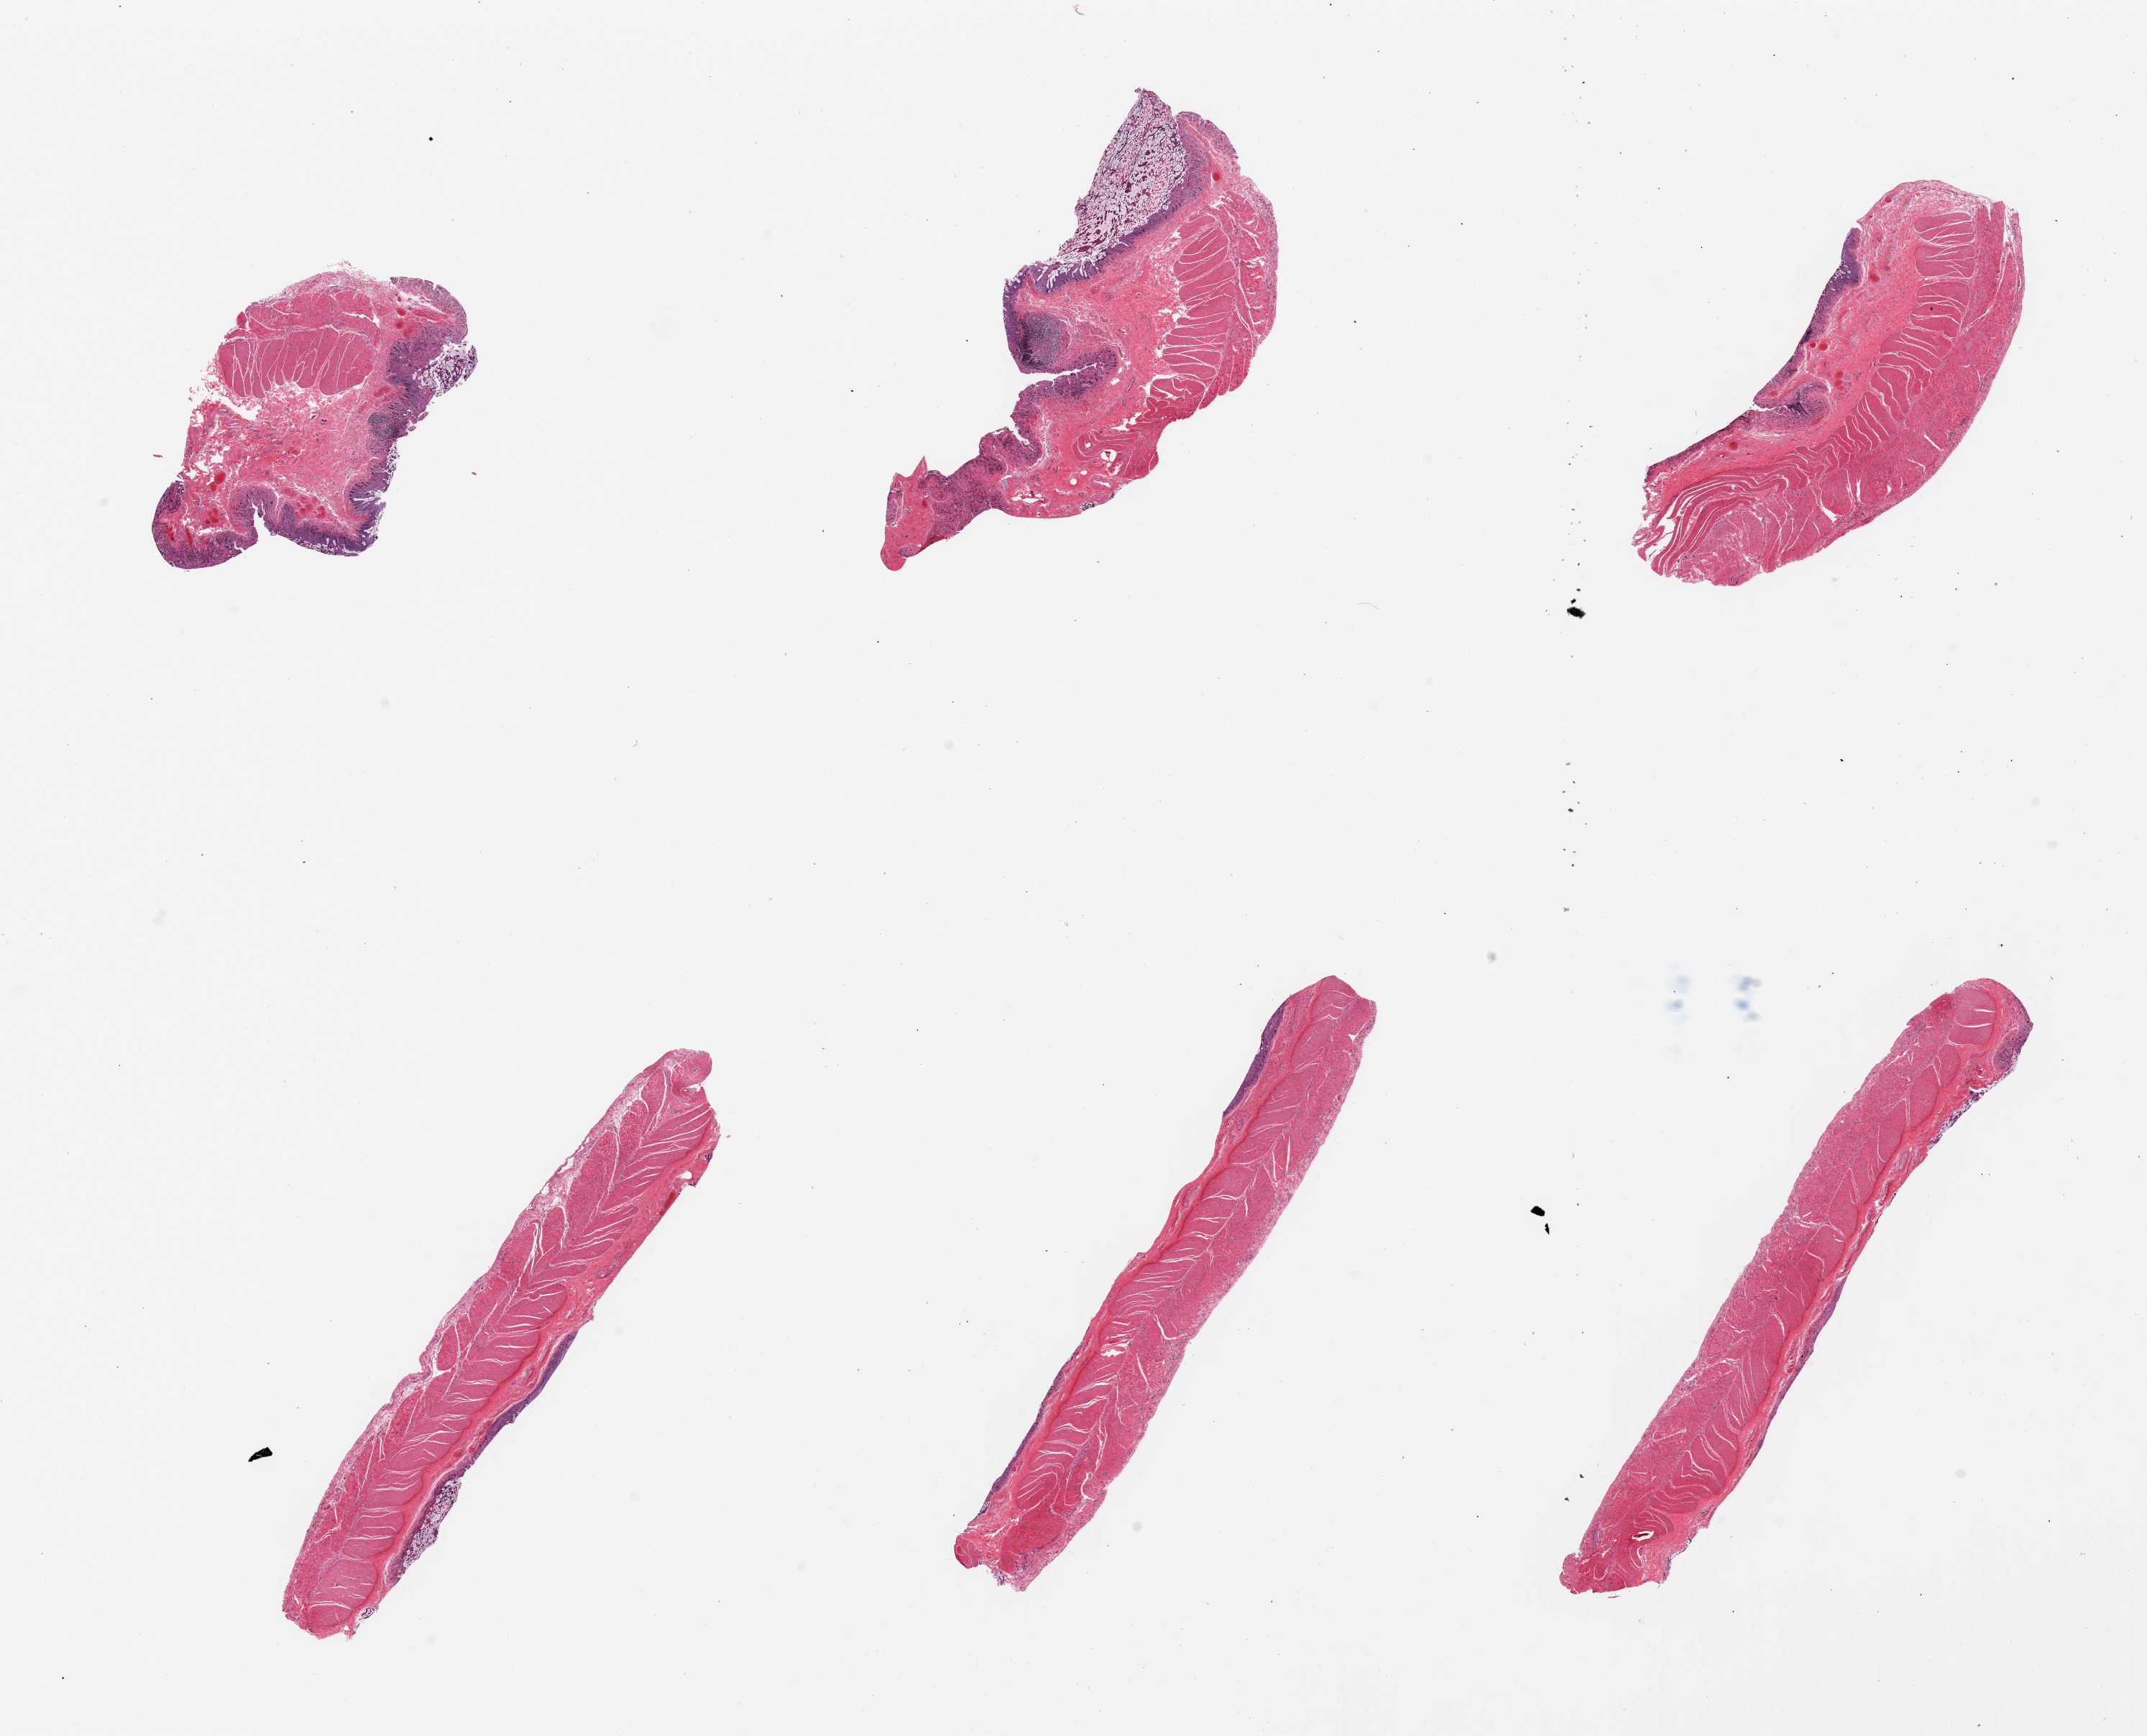
Hematoxylin and eosin (H&E) whole-slide image — a low-resolution overview of the entire scanned area, about 23.6 x 19.1 mm. PAXgene-fixed, paraffin-embedded tissue. Section of ileum (target tissue). Tissue donor sample. Donor: female.
Pathologist's review note for this sample: 4 pieces, mucosa autolyzed, ~15% lymphoid elements.